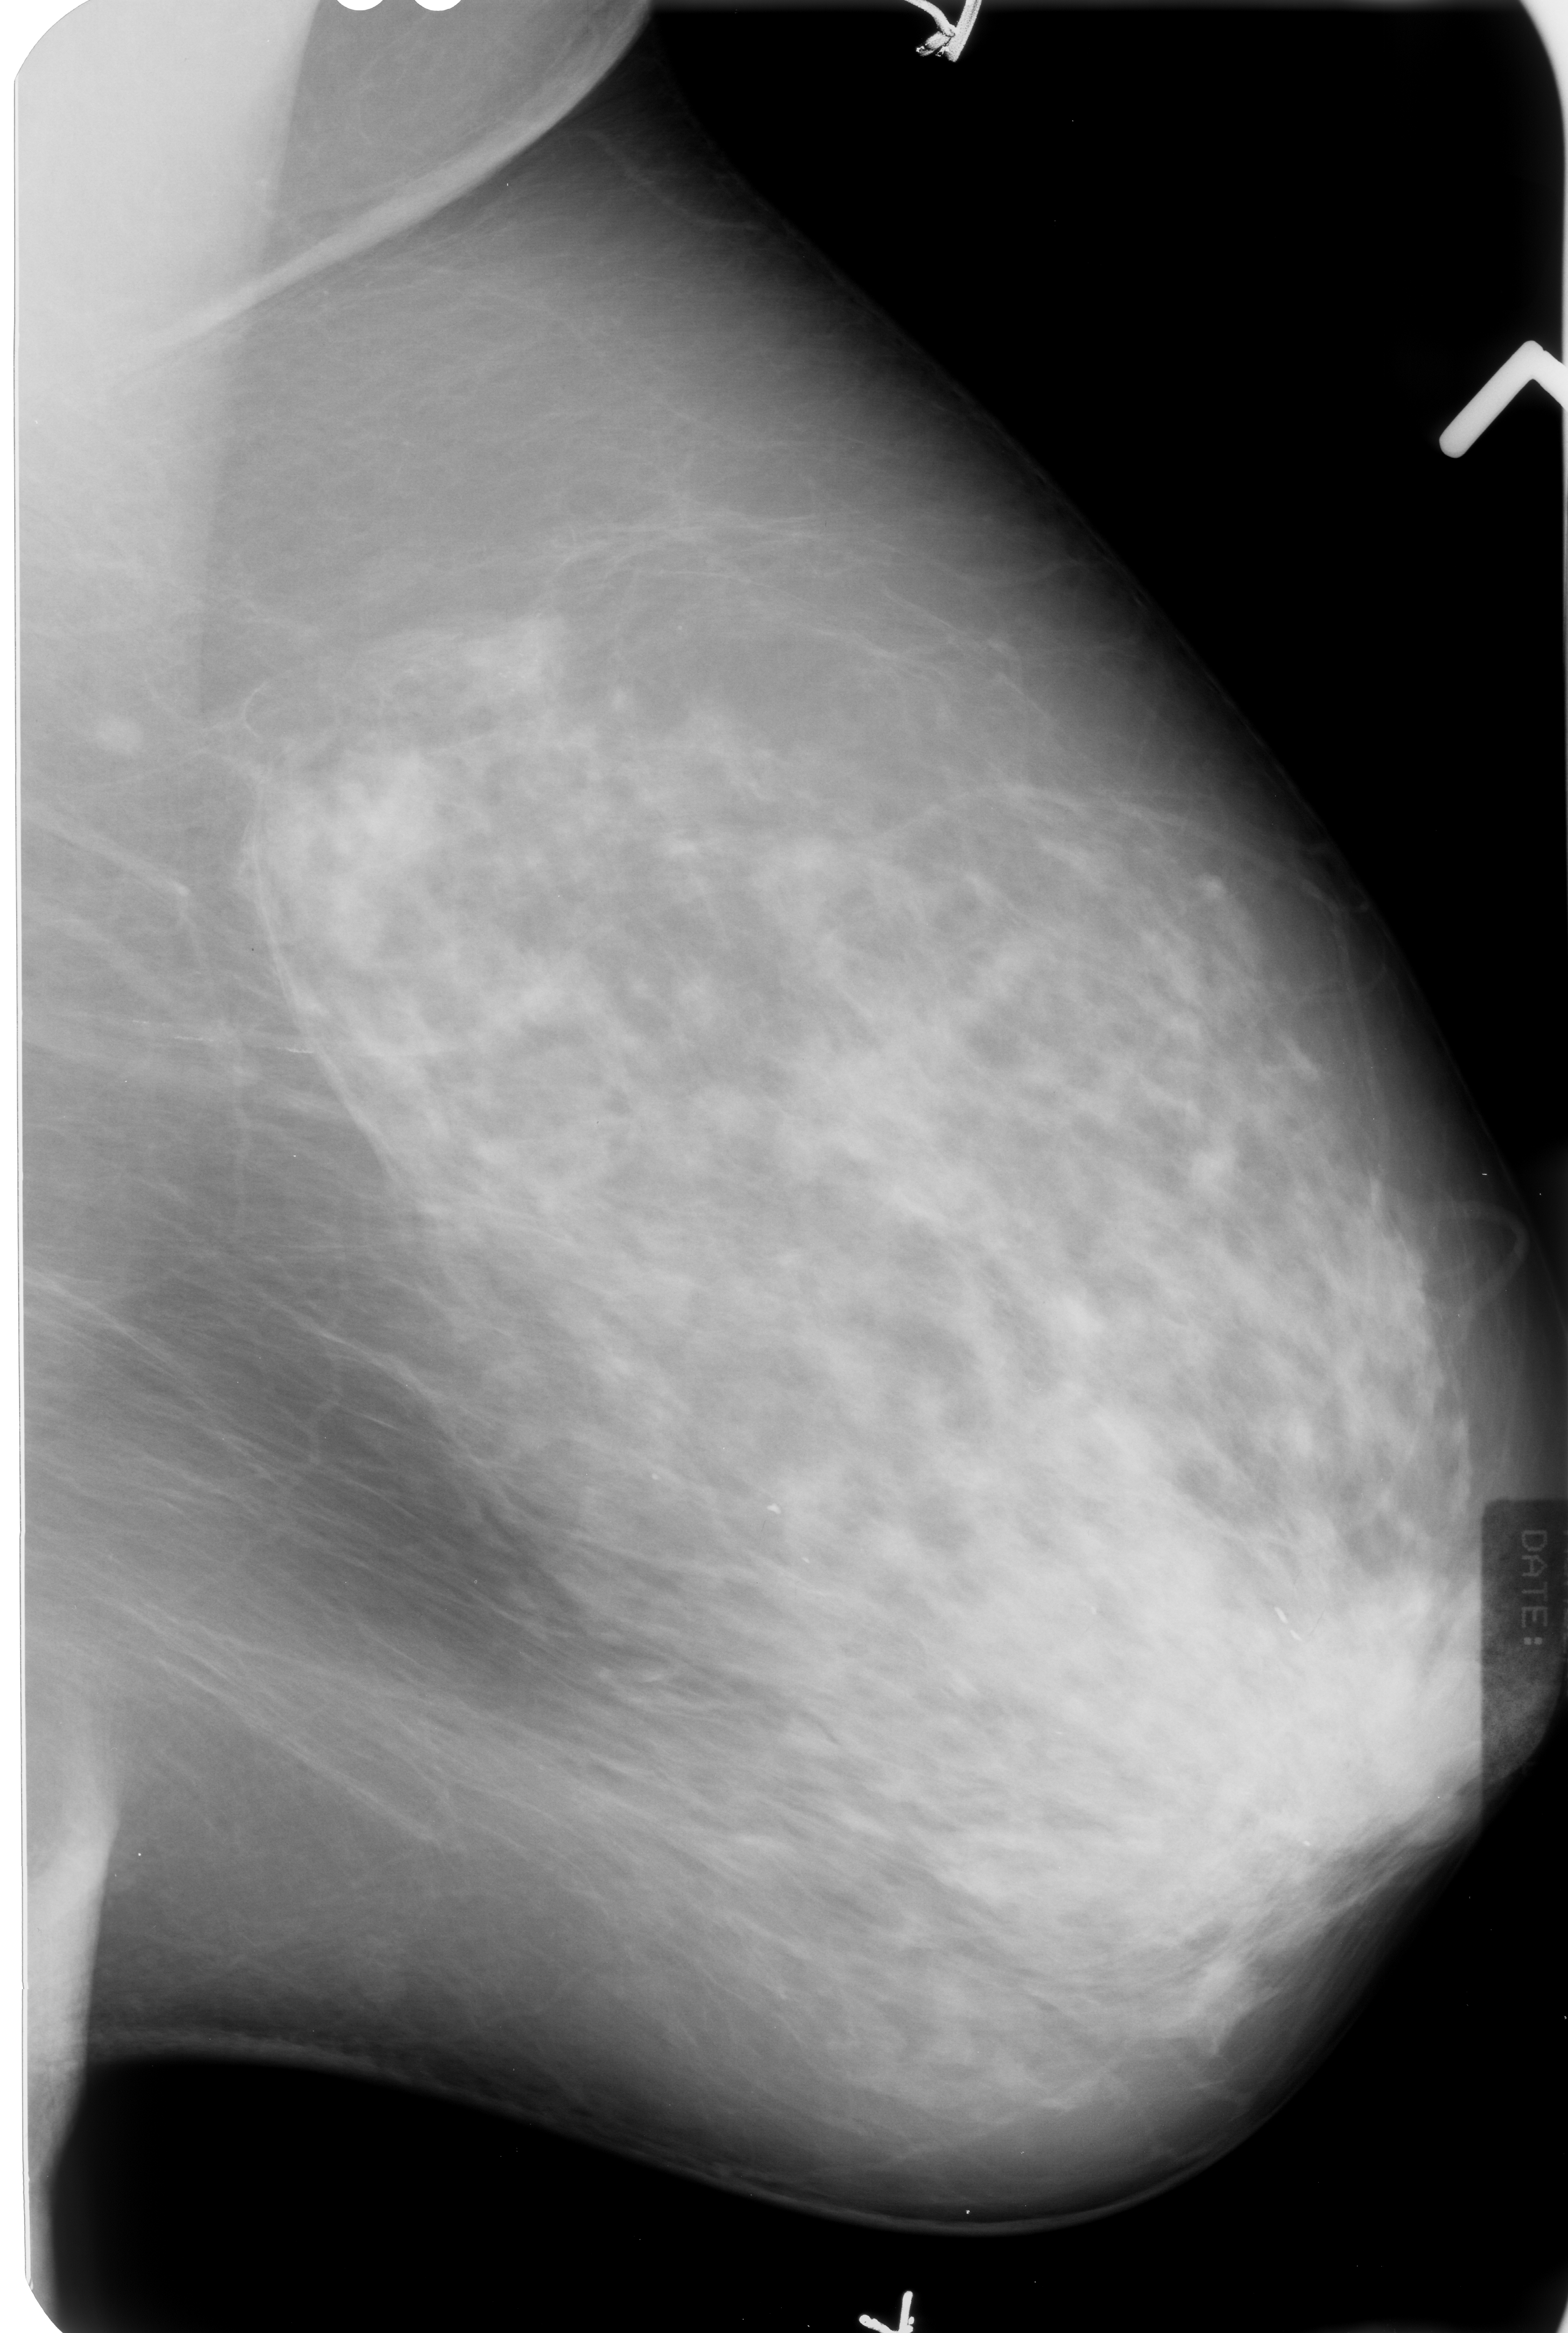
Digitized screen-film mammogram, left breast, mediolateral oblique (MLO) view, breast composition: heterogeneously dense (BI-RADS density category 3 of 4).
Marked findings (only marked abnormalities are described; nothing is implied about the rest of the image): Finding 1 of 3: calcifications, morphology vascular / coarse; BI-RADS assessment category 2; subtlety rating 3 on a 1 (subtle) to 5 (obvious) scale; benign without callback (not worked up further). Finding 2 of 3: calcifications, morphology vascular / coarse; BI-RADS assessment category 2; benign; no additional work-up was recommended (benign without callback). Finding 3 of 3: calcifications, morphology vascular / coarse; BI-RADS assessment category 2; subtlety rating 3 on a 1 (subtle) to 5 (obvious) scale; benign without callback (not worked up further).